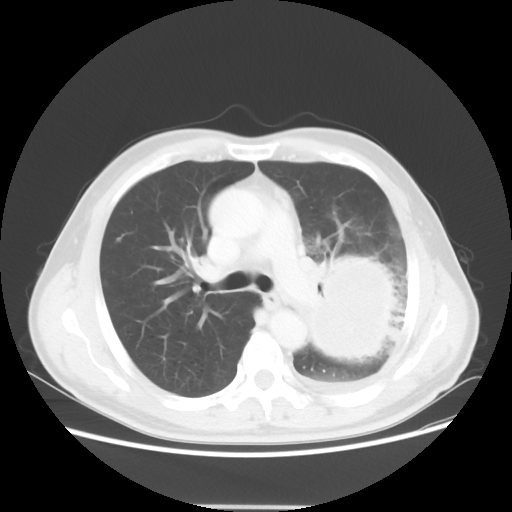
Chest CT, one axial slice. 100 kVp. Lung window (W 1500 / L -600 HU). 5 mm slice thickness. 512 × 512 image matrix, field of view 391 × 391 mm. Patient: male, 60 years. Case-level facts recorded for this patient, not image findings: clinical TNM (as recorded): T4 N1 M1a.
Structures marked on this image (bounding box drawn by a radiologist):
- lung tumour (recorded histology: large cell carcinoma): box from (x=311, y=250) to (x=398, y=365) px